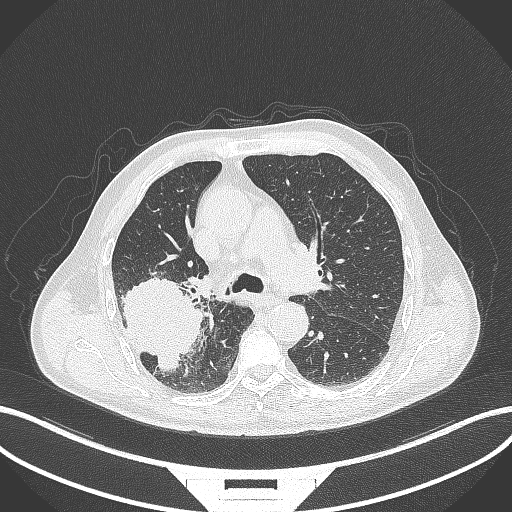
Chest CT, one axial slice; slice 263 of 429 in the series (ordered by position); 120 kVp; lung window (W 1500 / L -600 HU); 512 × 512 image matrix, field of view 400 × 400 mm. Patient: male, 72 years. From the clinical record (not read from this slice): clinical TNM (as recorded): T3 N2 M0.
Outlined on this slice (rectangle marked by the reading radiologist):
- lung tumour (recorded histology: adenocarcinoma): bounding box [x1, y1, x2, y2] px = [115, 276, 208, 369]